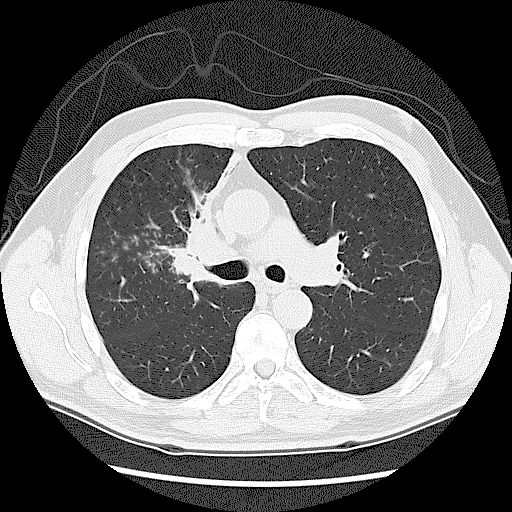
Low-dose screening chest CT, axial slice; first (baseline) screen; lung window (W 1500 / L -600 HU); lung (sharp) reconstruction kernel (LUNG). Male, age 60 years at enrolment.
Expert-annotated lung lesion, bounding box <158,220,242,313> (left, top, right, bottom; pixels). Screening reader's record for this exam: no non-calcified nodule ≥4 mm recorded. Official screen result: negative screen, significant abnormalities not suspicious for lung cancer.